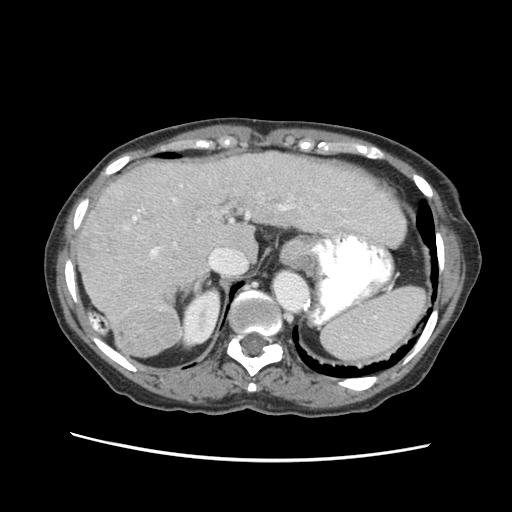
Contrast-enhanced abdominal CT (liver protocol), one axial slice; position 43 of 63 along the scan axis; reconstruction kernel STANDARD; 120 kVp; soft-tissue window (W 400 / L 40 HU); 2.5 mm slice thickness; 512 × 512 image matrix, field of view 340 × 340 mm. Case-level facts recorded for this patient, not image findings: diagnosis: hepatocellular carcinoma (patient treated with transarterial chemoembolisation; whether this scan precedes or follows treatment is not stated here); TNM stage (as recorded): Stage-I; Child-Pugh class: B; tumour differentiation: well differentiated; tumour nodularity: uninodular.
Annotated regions visible in this slice (semi-automatic segmentation, software-assisted and operator-edited):
- liver parenchyma outside the tumour (the mass and vessels are separate outlines, so this box may not span the whole liver): bounding box <76,148,404,356> (left, top, right, bottom; pixels)
- mass: <112,301,180,355>
- liver vessels: <131,185,335,257>